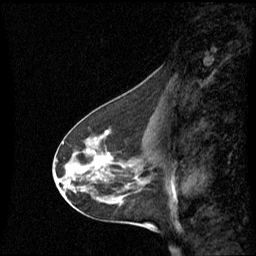
Breast MRI (dynamic contrast-enhanced), one sagittal slice. Position 30 of 60 along the scan axis. Dynamic contrast-enhanced series, image 2 of 3 at this slice position (ordered by acquisition). 1.5 T. TE 4.2 ms, TR 8.4 ms. 2.2 mm slice thickness. 256 × 256 image matrix. Female patient, age 45 years. Case-level facts recorded for this patient, not image findings: setting: breast cancer imaged before/during neoadjuvant chemotherapy; receptor status: HR-positive, HER2-negative.
Structures marked on this image (semi-automatic segmentation, software-assisted and operator-edited):
- analysis volume of interest (the breast-tissue region the enhancement analysis was run in; not a lesion): bounding box (x1, y1, x2, y2) in pixels: (60, 126, 149, 215)
- tumour enhancement mask (voxels above the 70 % enhancement threshold inside the analysis volume of interest): (92, 132, 108, 169)